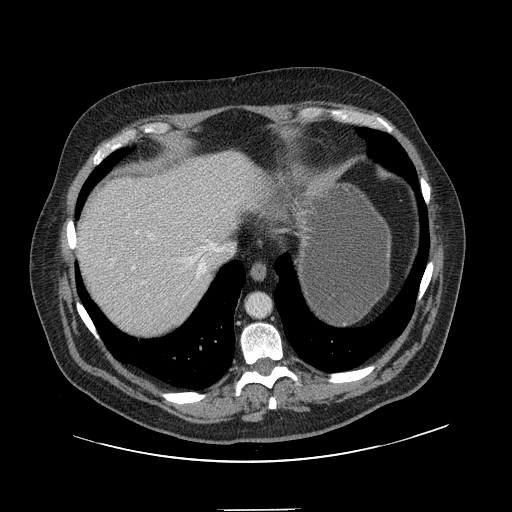
Contrast-enhanced abdominal CT, one axial slice. Slice 126 of 154 in the series (ordered by position). Soft-tissue window (W 400 / L 40 HU). 2.5 mm slice thickness. 512 × 512 image matrix, field of view 451 × 451 mm. Male patient, age 61 years. Case-level facts recorded for this patient, not image findings: diagnosis: colorectal cancer liver metastases, imaged before liver resection; multiple liver metastases: yes; largest metastasis: 2.6 cm; disease in both lobes: yes.
Structures marked on this image (expert manual segmentation):
- hepatic veins: bounding box (x1, y1, x2, y2) in pixels: (111, 241, 222, 283)
- liver: (77, 152, 256, 337)
- planned liver remnant (the part of the liver to remain after resection): (77, 152, 256, 337)
- portal vein (with intrahepatic branches): (127, 214, 144, 284)